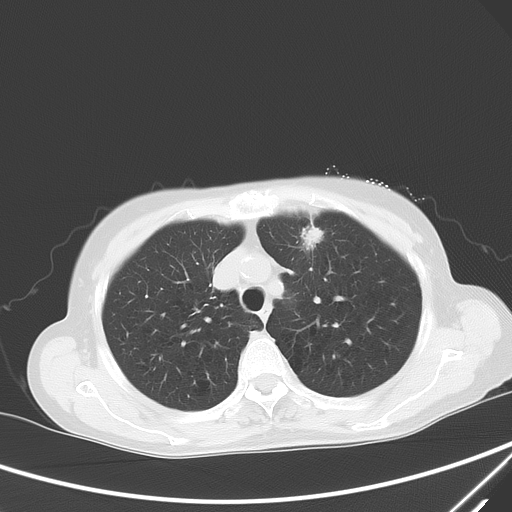
Chest CT, one axial slice. Position 47 of 60 along the scan axis. Lung window (W 1500 / L -600 HU). 512 × 512 image matrix, field of view 350 × 350 mm. Female patient, age 71 years. Case-level facts recorded for this patient, not image findings: clinical TNM (as recorded): T1c N0 M0; histopathological grade: G2-3.
Outlined on this slice (rectangle marked by the reading radiologist):
- lung tumour (recorded histology: adenocarcinoma): bounding box (x1, y1, x2, y2) in pixels: (296, 221, 327, 253)